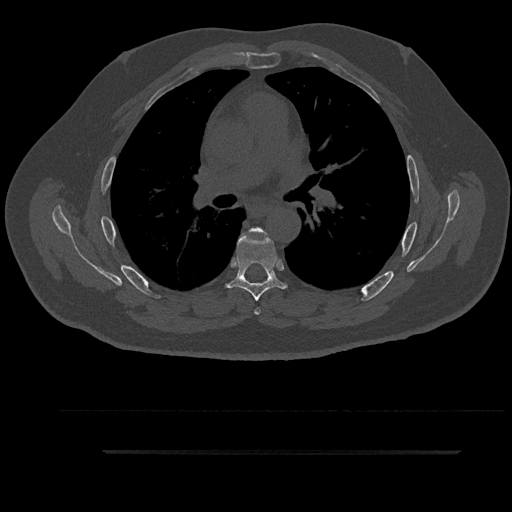
CT including the spine, one axial slice; slice 585 of 797 in the series (ordered by position); reconstruction kernel Br40s/3; 120 kVp; bone window (W 1800 / L 400 HU); 0.5 mm slice thickness; 512 × 512 image matrix, field of view 432 × 432 mm. Patient: male, 63 years. From the clinical record (not read from this slice): primary cancer: renal.
Outlined on this slice (semi-automatically segmented with operator editing):
- T5 vertebra: bounding box <242,228,269,315> (left, top, right, bottom; pixels)
- T6 vertebra: <226,231,286,301>